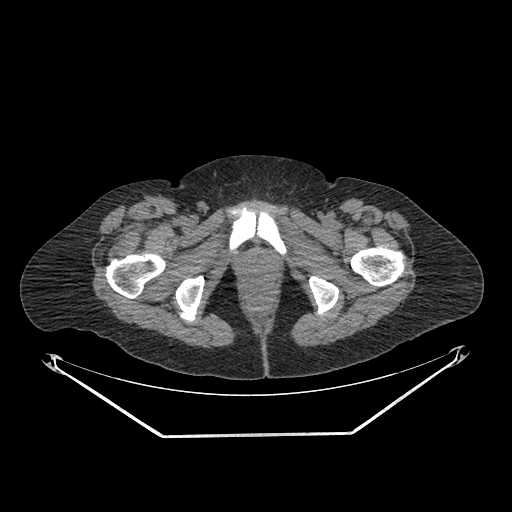
CT of an extremity soft-tissue mass (from a PET/CT study), one axial slice; slice 286 of 311 in the series (ordered by position); reconstruction kernel SOFT; soft-tissue window (W 400 / L 40 HU); 3.75 mm slice thickness; 512 × 512 image matrix, field of view 500 × 500 mm. Female patient. From the clinical record (not read from this slice): histological type: pleiomorphic undifferentiated sarcoma; grade: high; site of the primary tumour: right quadricep.
Outlined on this slice (expert contour drawn on MRI and transferred to this co-registered scan by the dataset authors):
- tumour plus oedema (research contour): box from (x=109, y=231) to (x=136, y=268) px